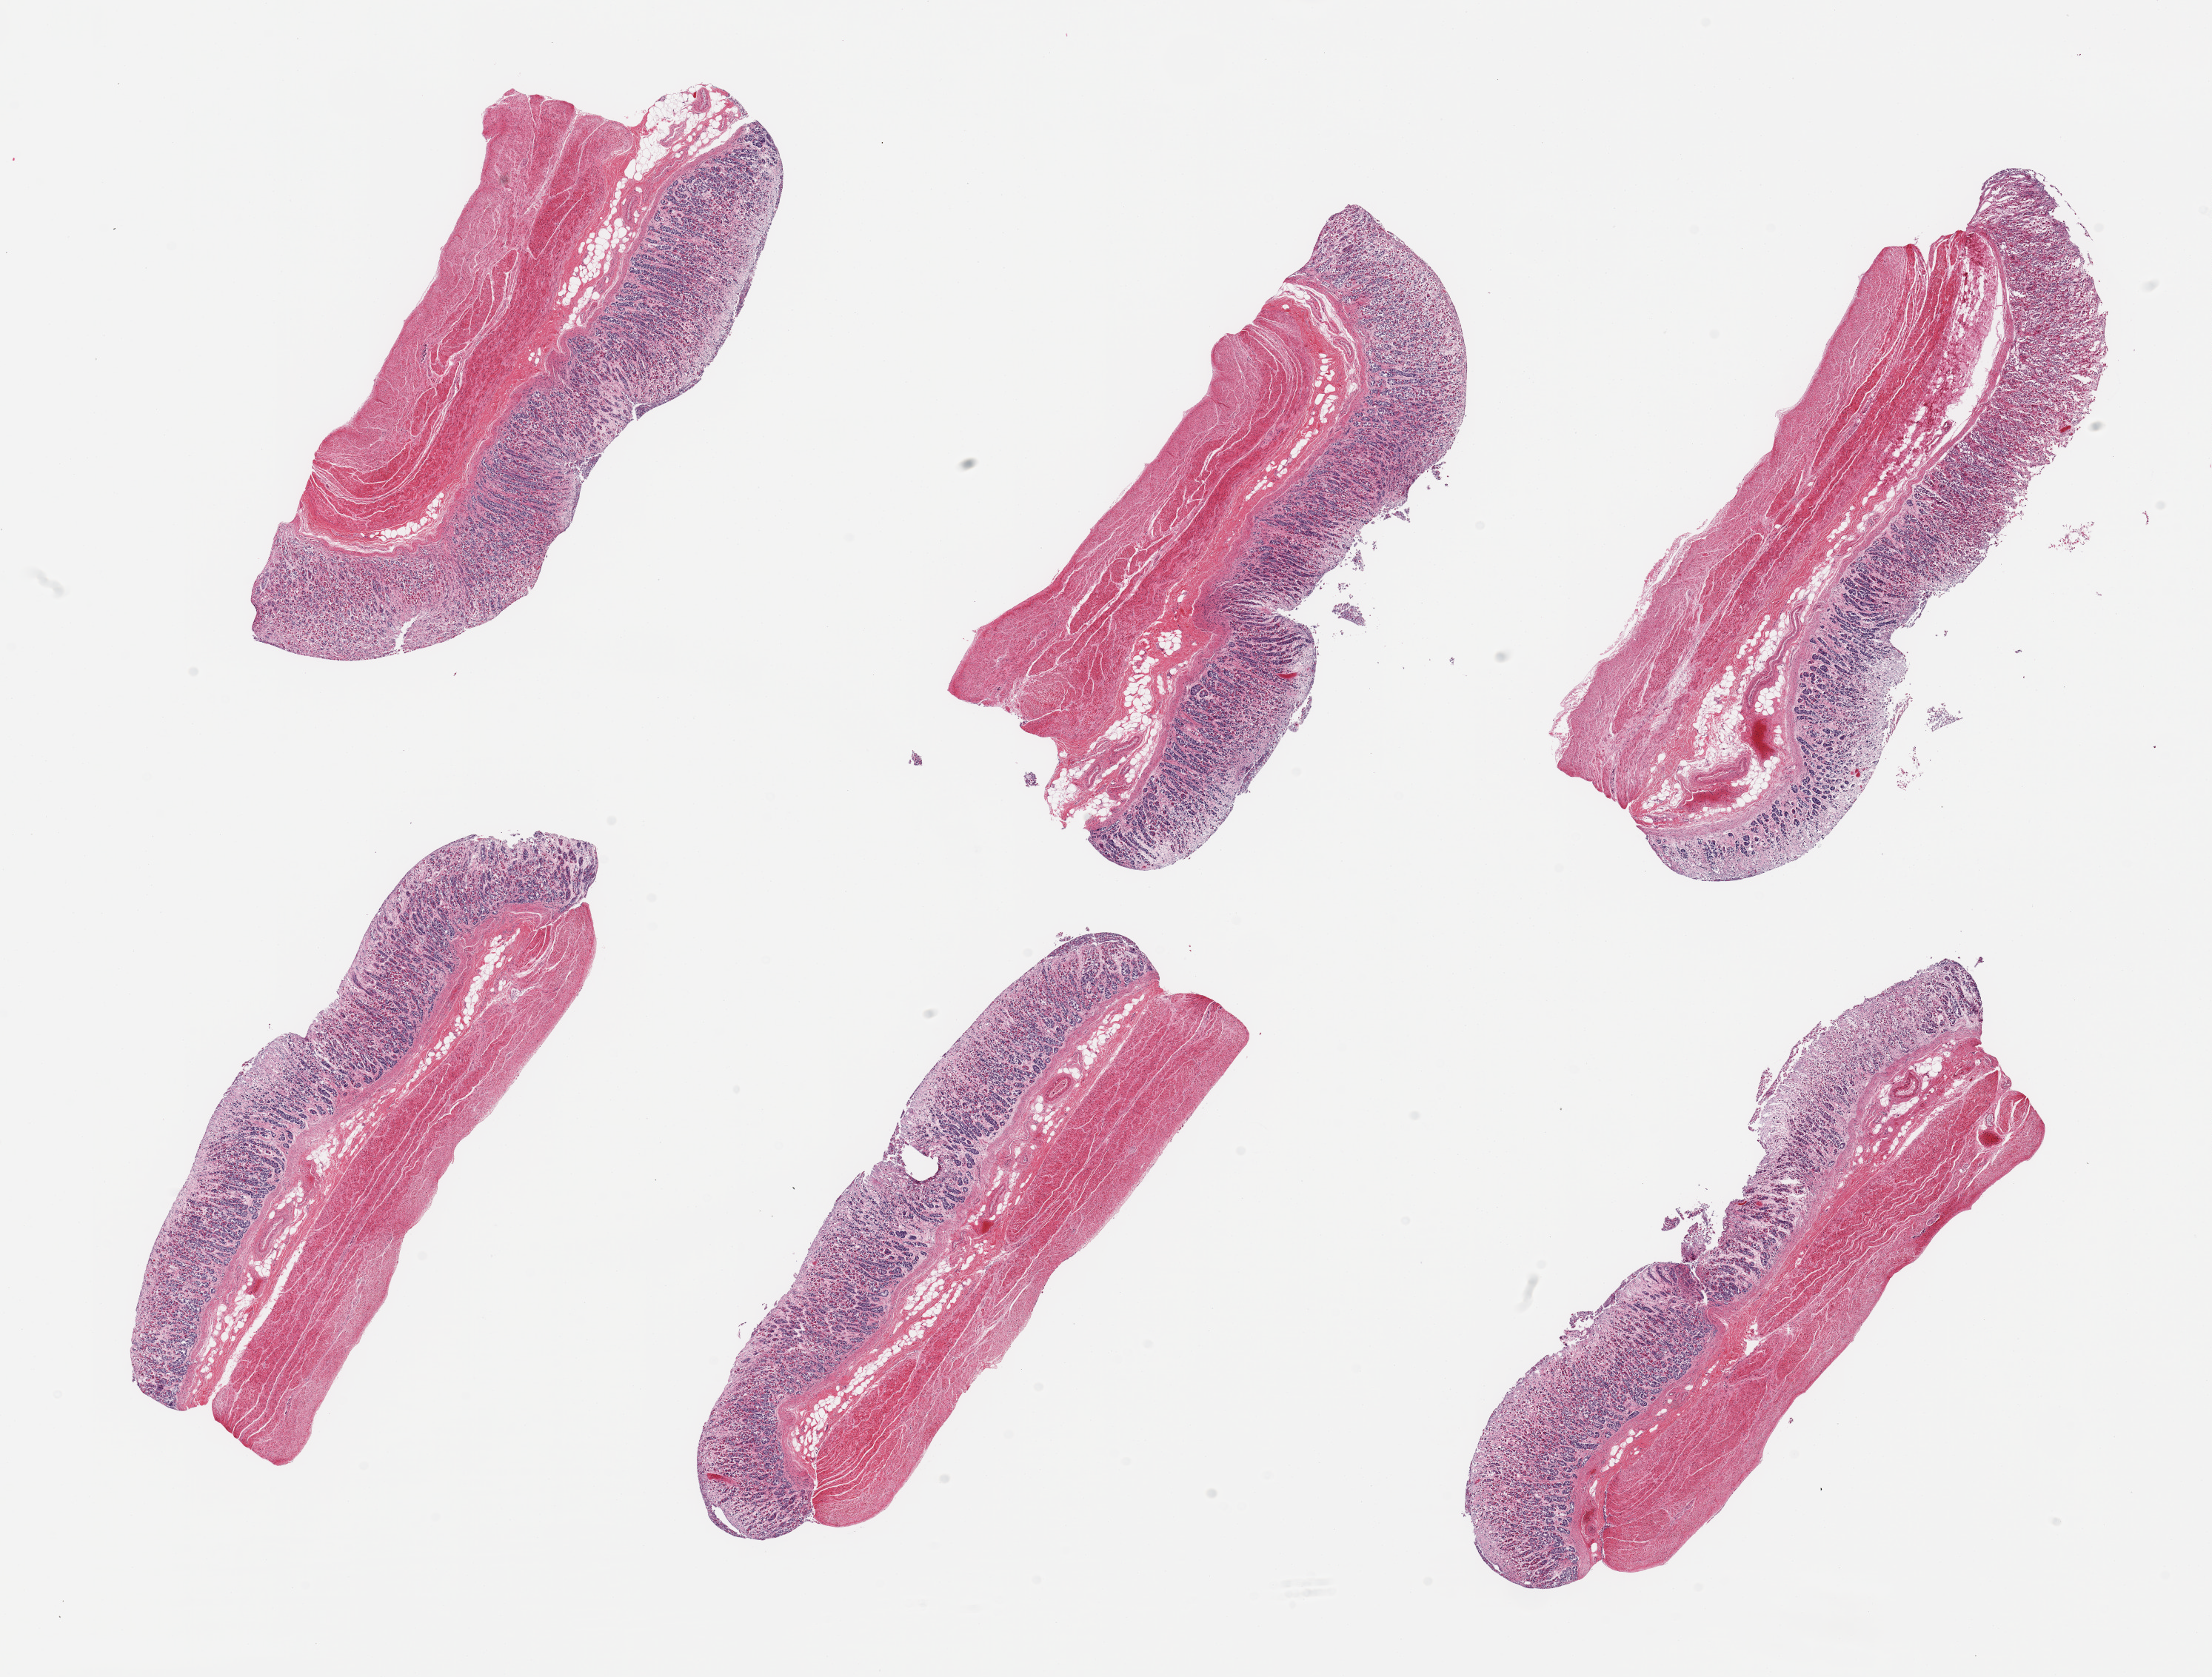
Digitized haematoxylin and eosin-stained section, low-resolution overview of the scanned area, about 23.6 x 17.9 mm, PAXgene-fixed paraffin-embedded (PFPE) section, section of stomach (target tissue), donor tissue sample. Donor sex: male.
- pathologist's review note for this sample: 6 pieces, mucosa up to ~1mm, ~40% thickness, moderate autolysis